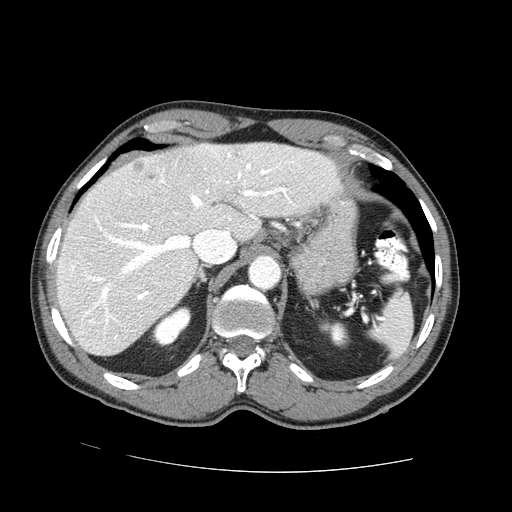
Contrast-enhanced abdominal CT (liver protocol), one axial slice. Slice 52 of 73 in the series (ordered by position). One of 2 acquisitions stored at this slice position. Soft-tissue window (W 400 / L 40 HU). 2.5 mm slice thickness. 512 × 512 image matrix. From the clinical record (not read from this slice): diagnosis: hepatocellular carcinoma (patient treated with transarterial chemoembolisation; whether this scan precedes or follows treatment is not stated here); TNM stage (as recorded): Stage-IVA; Child-Pugh class: A; tumour differentiation: no biopsy; tumour nodularity: uninodular.
Structures marked on this image (semi-automatic segmentation, software-assisted and operator-edited):
- liver parenchyma outside the tumour (the mass and vessels are separate outlines, so this box may not span the whole liver): bounding box <56,142,342,356> (left, top, right, bottom; pixels)
- mass: <133,161,154,179>
- liver vessels: <72,147,291,323>